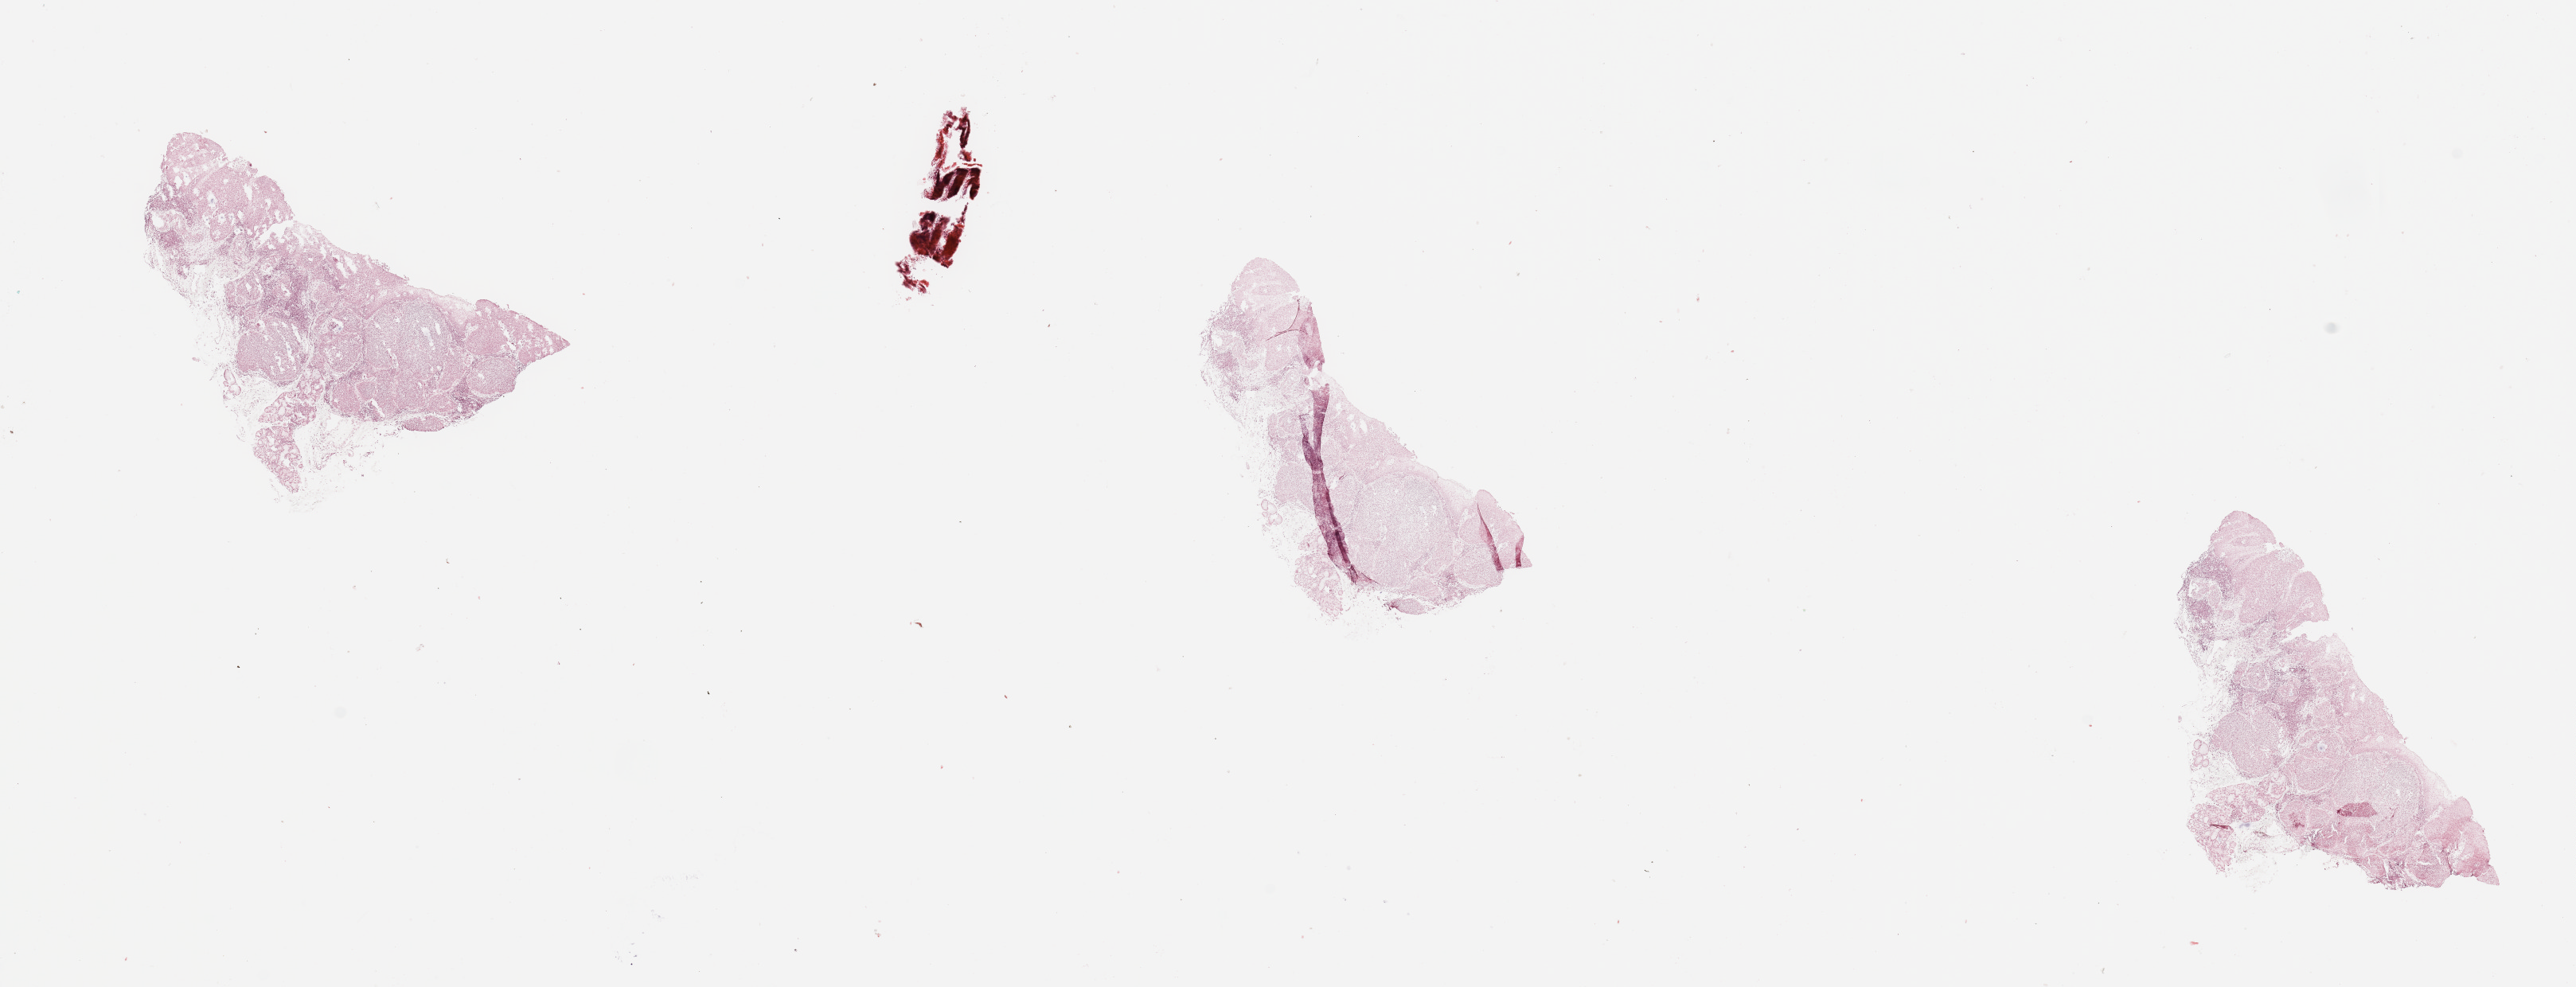
Digitized H&E-stained tissue section (whole slide), a low-resolution overview of the entire scanned area, about 25.6 x 9.8 mm (slide scanned at 20x); tumour tissue sample, sampled site: larynx. 63-year-old male patient. Histologic grade: G2 (moderately differentiated). Slide review estimates, as recorded: tumour nuclei 85%, necrosis 5%.
- AJCC pathologic stage: IVA
- primary tumour site (as recorded): larynx
- histologic diagnosis: Squamous cell carcinoma, NOS (larynx, NOS)